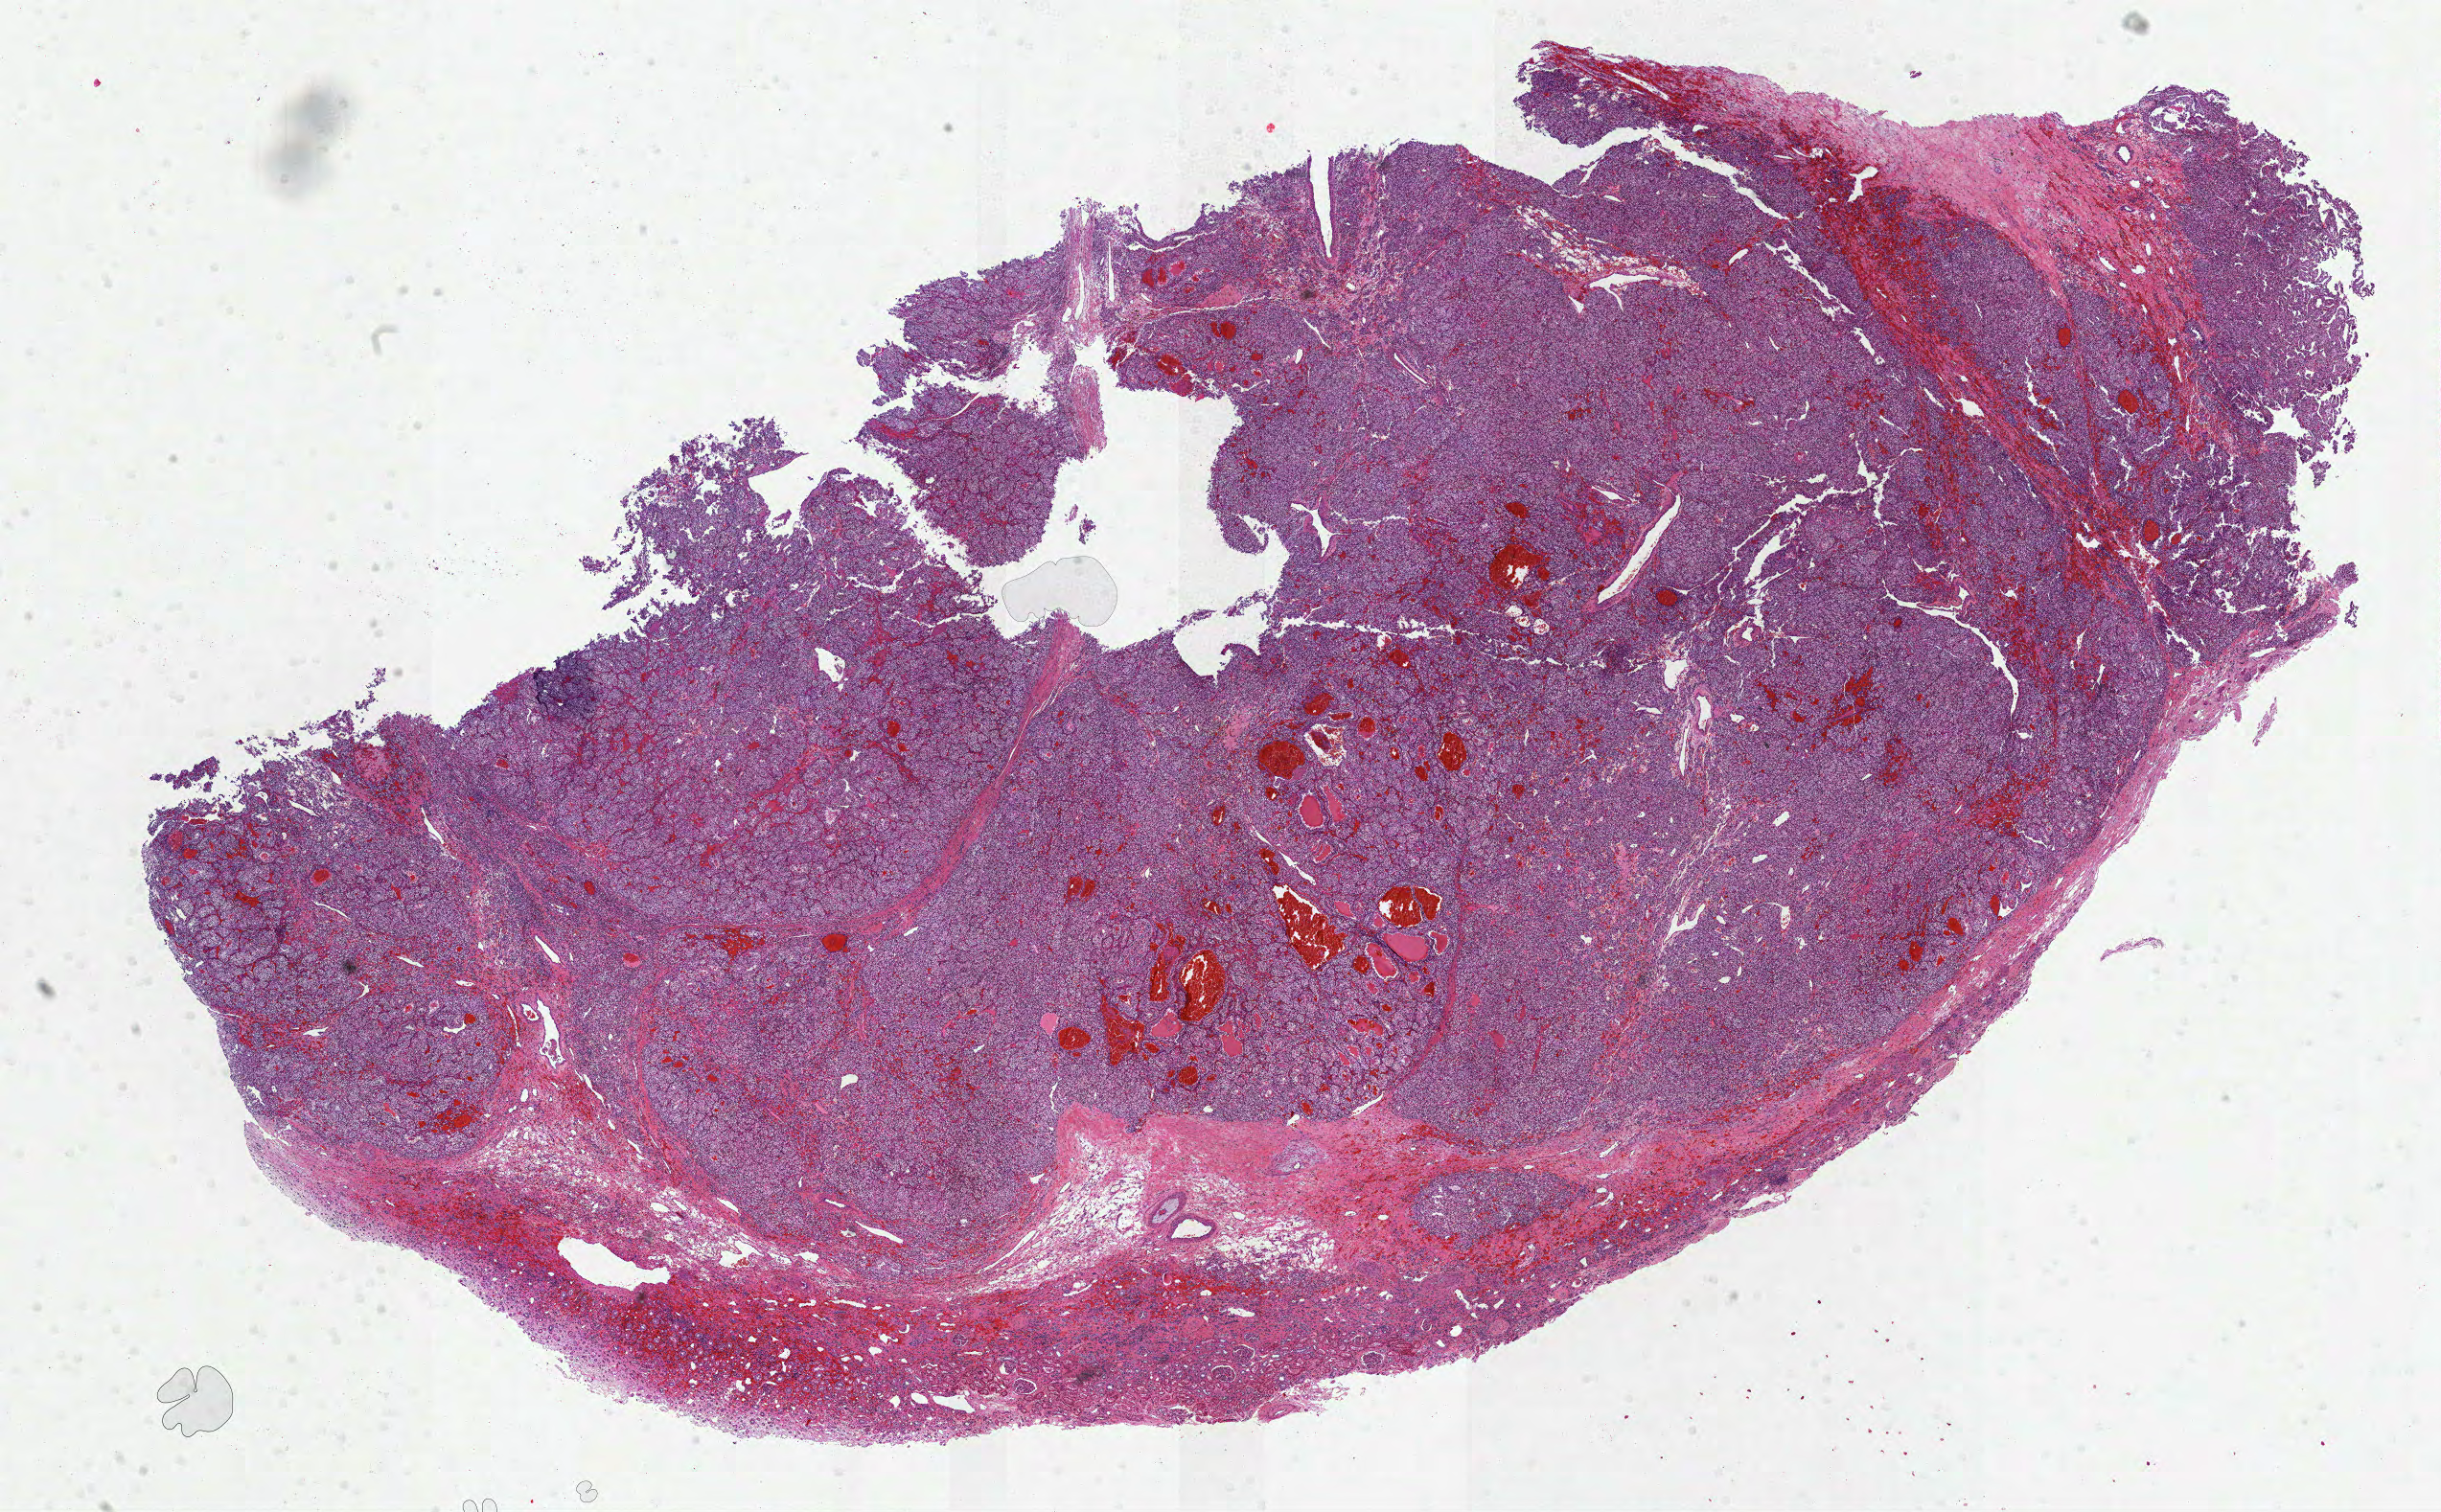
Digitized H&E tissue section (whole slide) — whole scanned area (about 20.5 x 12.7 mm, slide scanned at 40x) shown as a low-resolution overview; FFPE section; kidney, primary tumour sample. Female, age 52 years at initial diagnosis. Histologic grade: G2 (moderately differentiated).
AJCC pathologic stage: I. Histologic diagnosis: Clear cell adenocarcinoma, NOS. TNM: T1a NX M0.